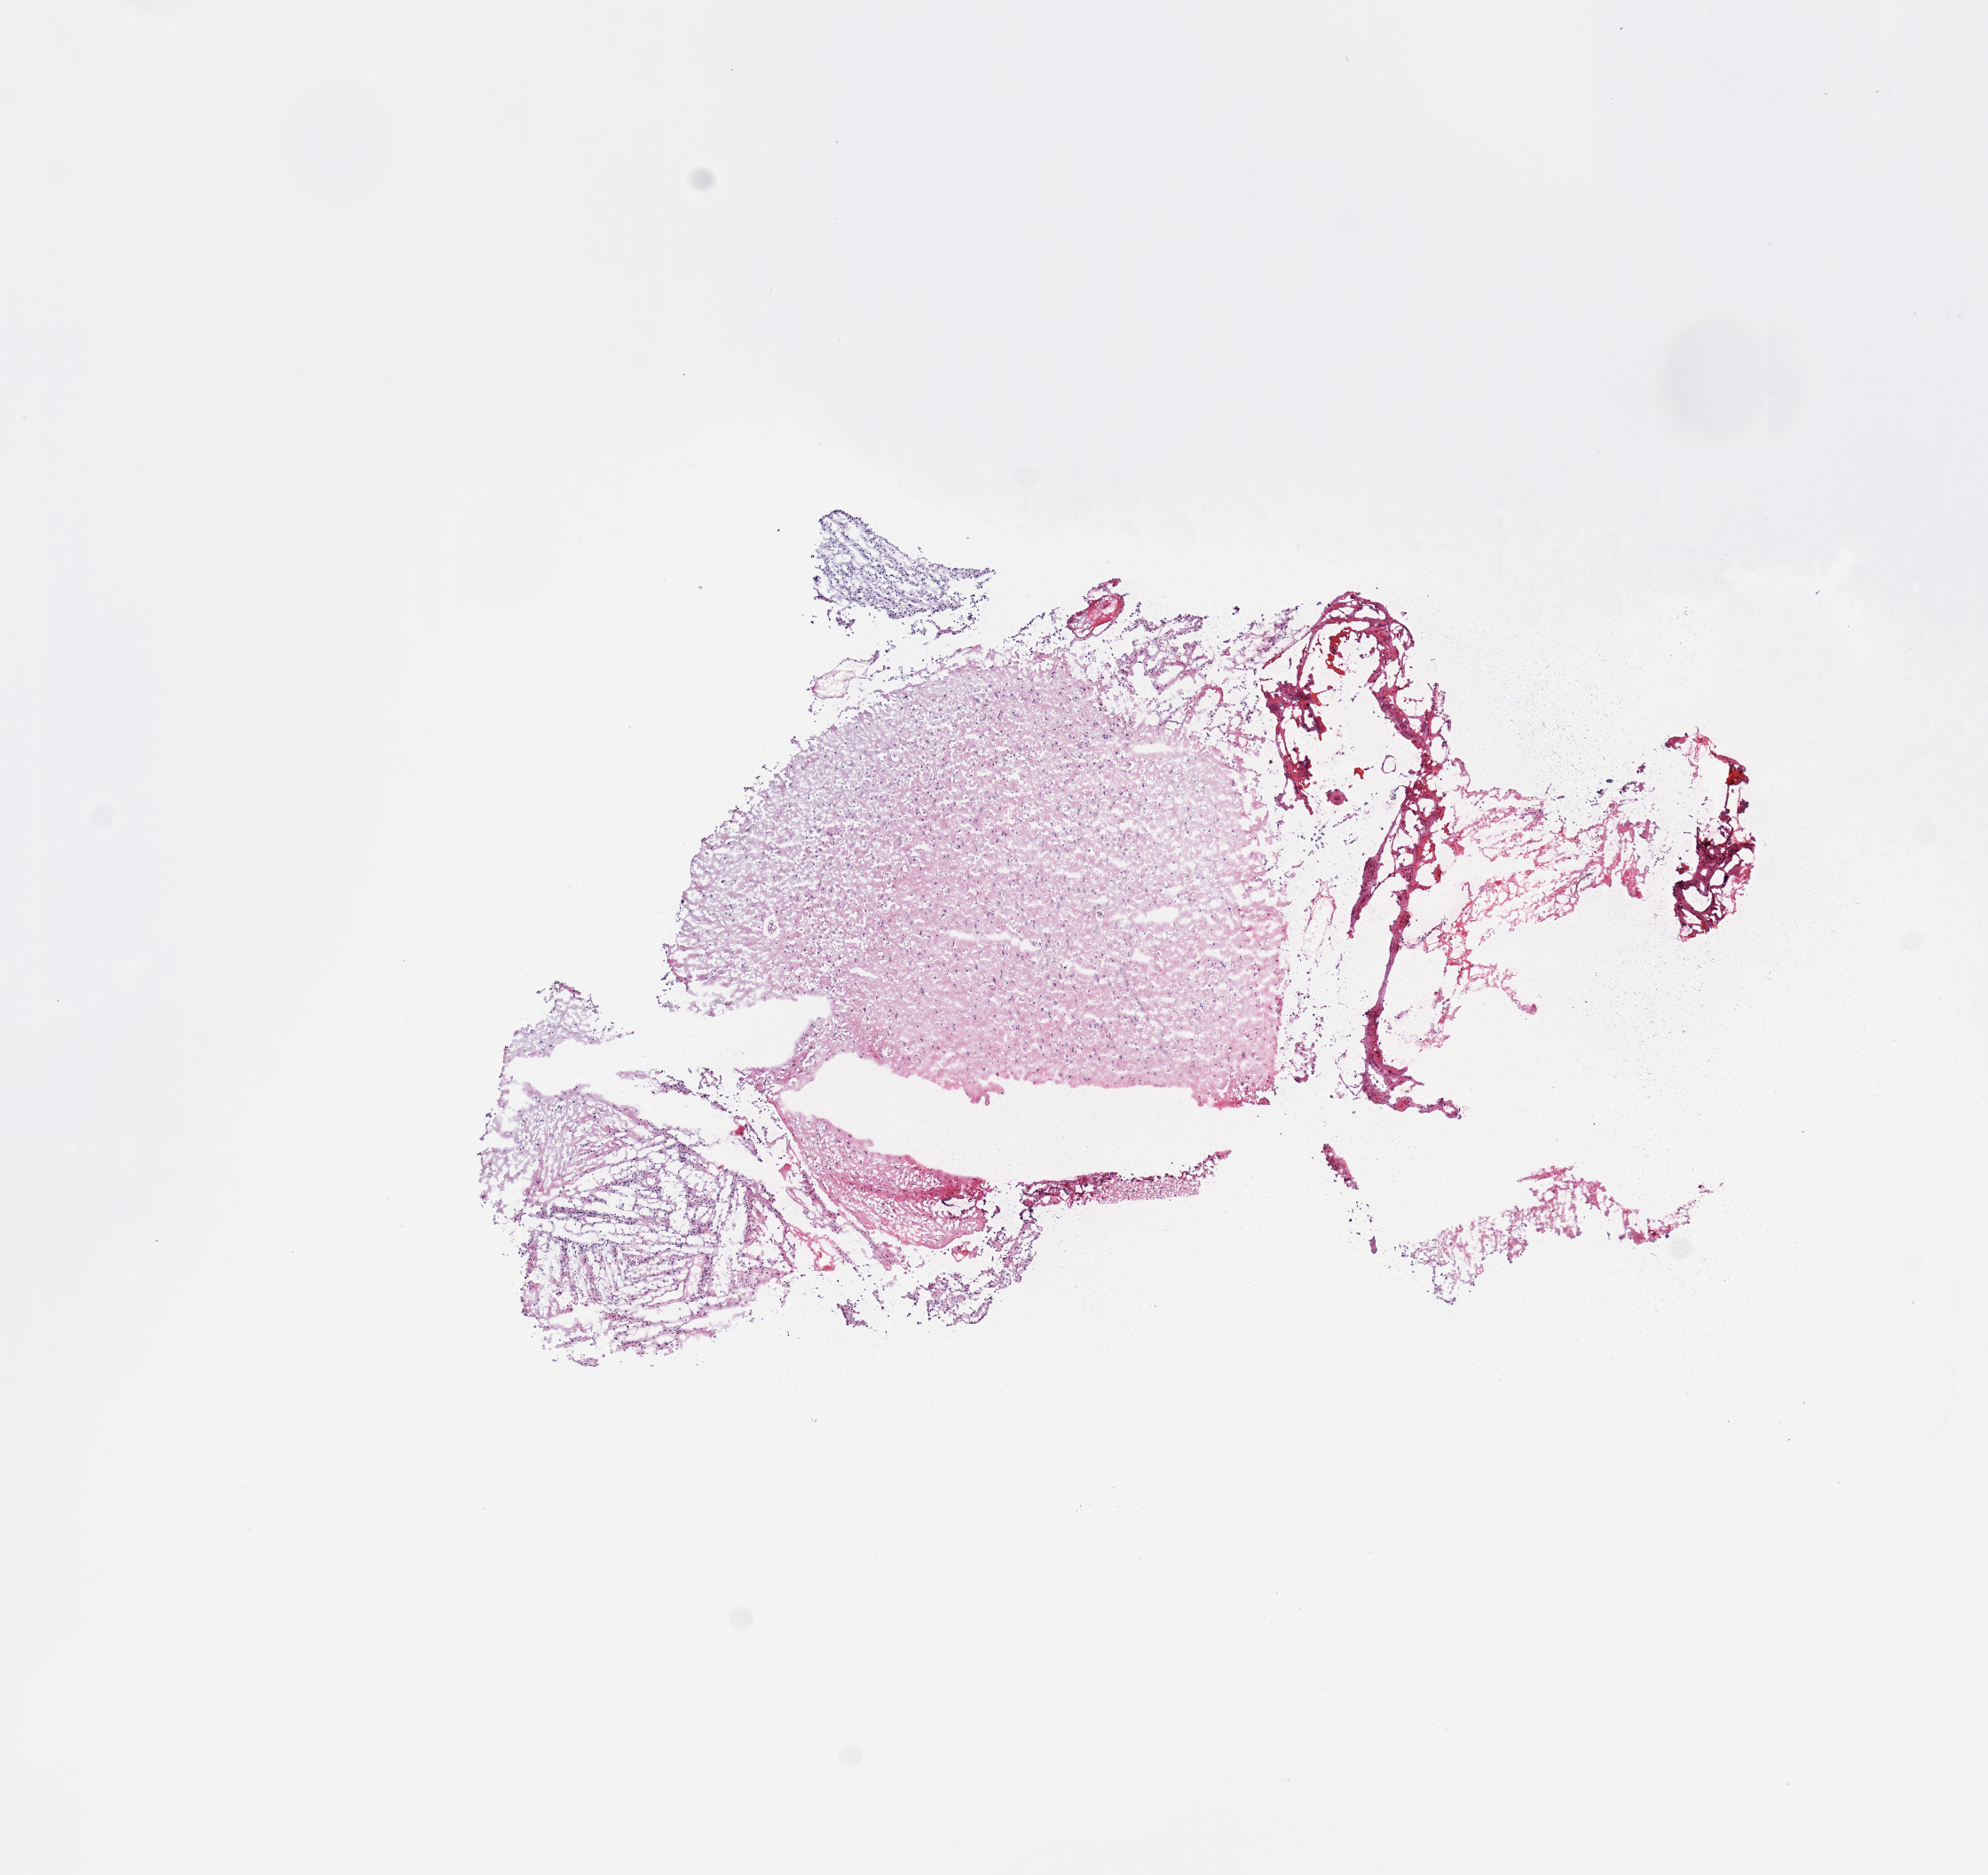
Digitized H&E tissue section (whole slide) — a low-resolution overview of the entire scanned area, about 8.9 x 8.4 mm, brain, tumour tissue. Patient: male, age 82 years.
• primary tumour site (as recorded): temporal lobe
• patient diagnosis (cohort enrolment): glioblastoma multiforme (brain)